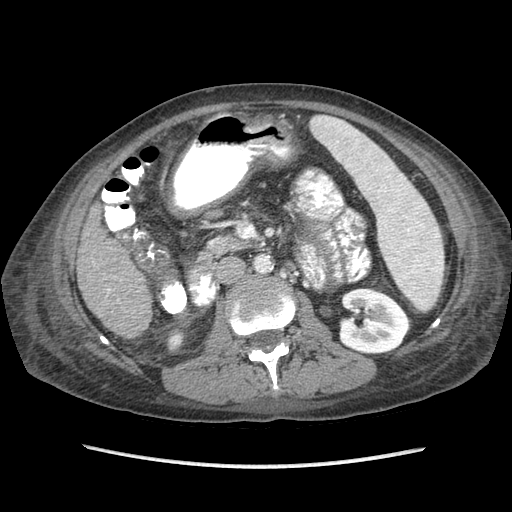
Contrast-enhanced abdominal CT (liver protocol), one axial slice; position 25 of 87 along the scan axis; reconstruction kernel STANDARD; 120 kVp; soft-tissue window (W 400 / L 40 HU); 2.5 mm slice thickness; 512 × 512 image matrix, field of view 340 × 340 mm. Case-level facts recorded for this patient, not image findings: diagnosis: hepatocellular carcinoma (patient treated with transarterial chemoembolisation; whether this scan precedes or follows treatment is not stated here); TNM stage (as recorded): Stage-IIIB; Child-Pugh class: A; tumour differentiation: no biopsy.
Outlined on this slice (semi-automatic segmentation, software-assisted and operator-edited):
- liver parenchyma outside the tumour (the mass and vessels are separate outlines, so this box may not span the whole liver): bounding box [x1, y1, x2, y2] px = [76, 202, 151, 336]